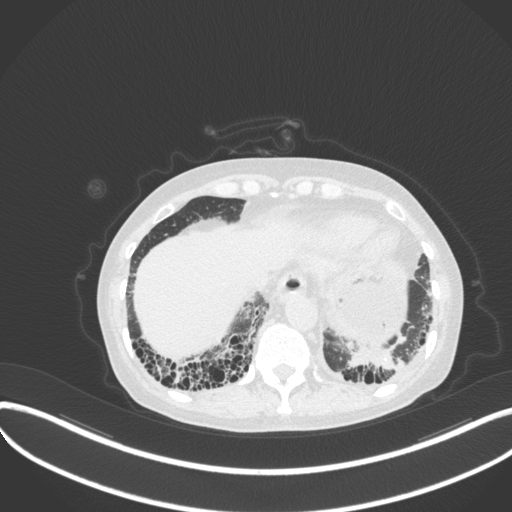
Chest CT, one axial slice. Slice 57 of 373 in the series (ordered by position). Reconstruction kernel B31f. Lung window (W 1500 / L -600 HU). 512 × 512 image matrix, field of view 400 × 400 mm. Patient: female, 56 years. Case-level facts recorded for this patient, not image findings: clinical TNM (as recorded): T1 N0 M0.
Structures marked on this image (bounding box drawn by a radiologist):
- lung tumour (recorded histology: adenocarcinoma): bounding box <340,343,407,380> (left, top, right, bottom; pixels)